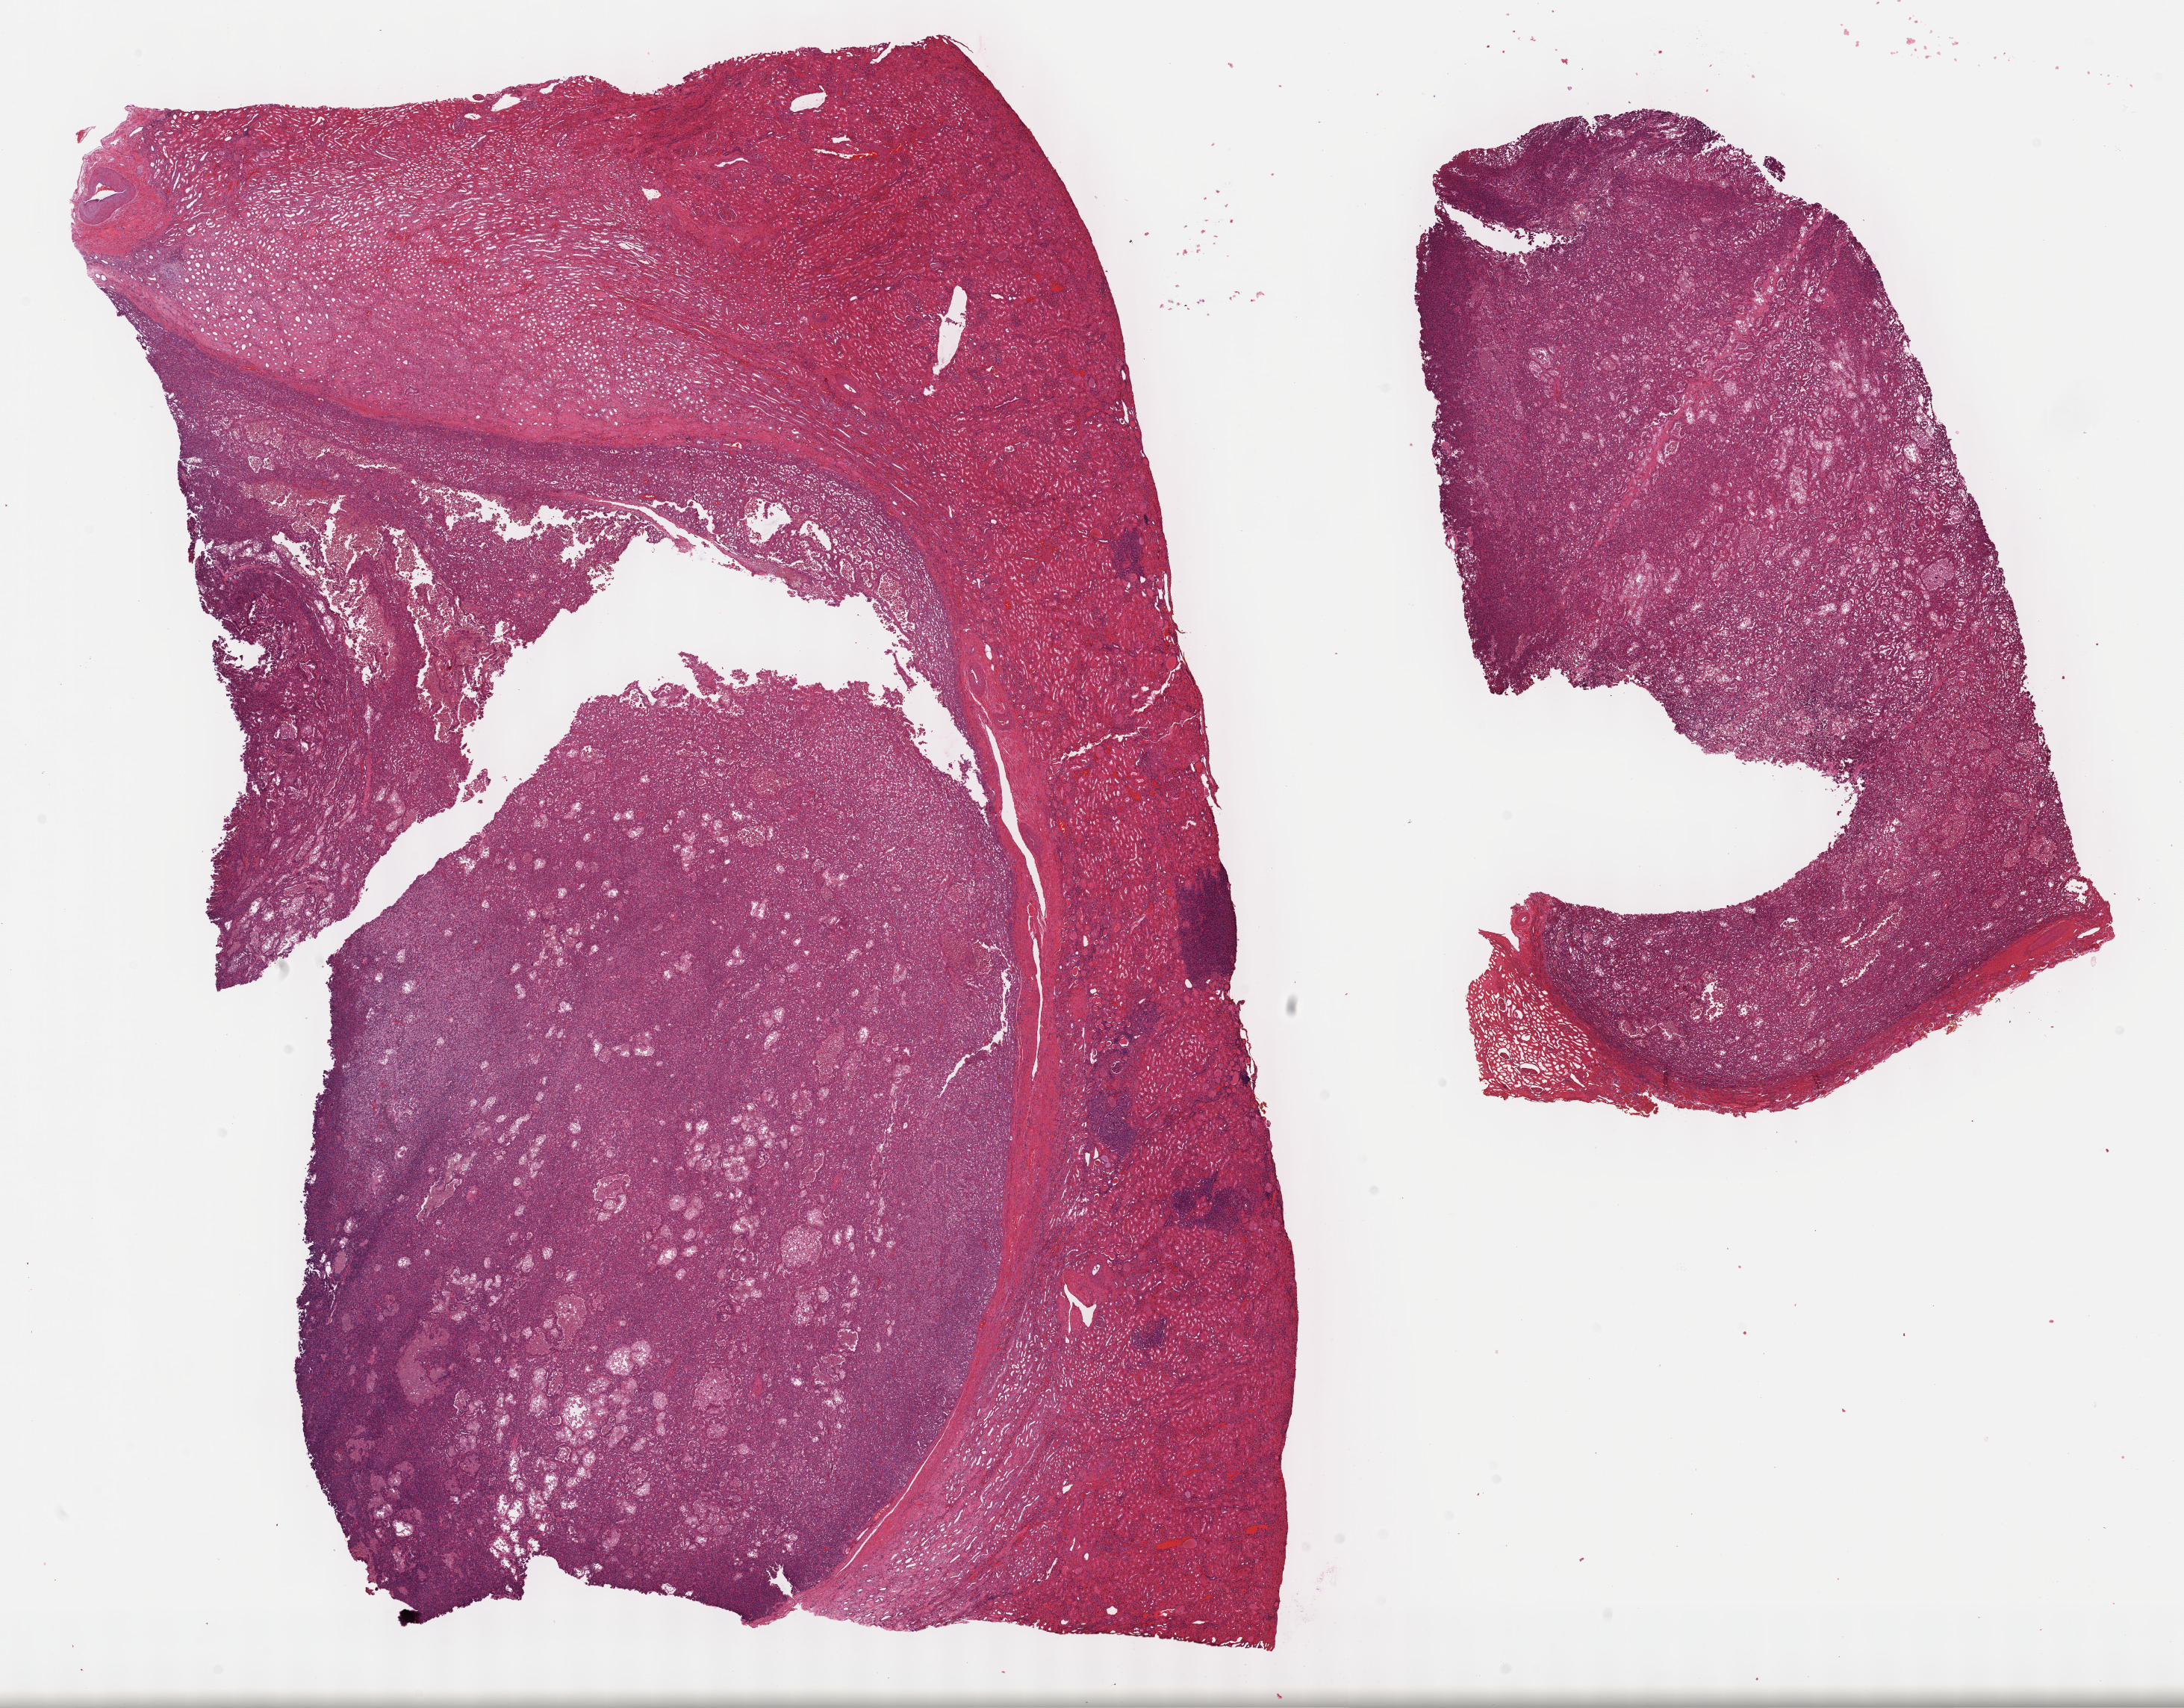
Digitized H&E tissue section (whole slide), whole scanned area (about 23.7 x 18.5 mm, acquisition: 40x scan) shown as a low-resolution overview. FFPE section. Sample: primary tumour, kidney. Male patient; age at initial diagnosis 63 years.
AJCC pathologic stage: I (7th edition). Diagnosis: Papillary adenocarcinoma, NOS.